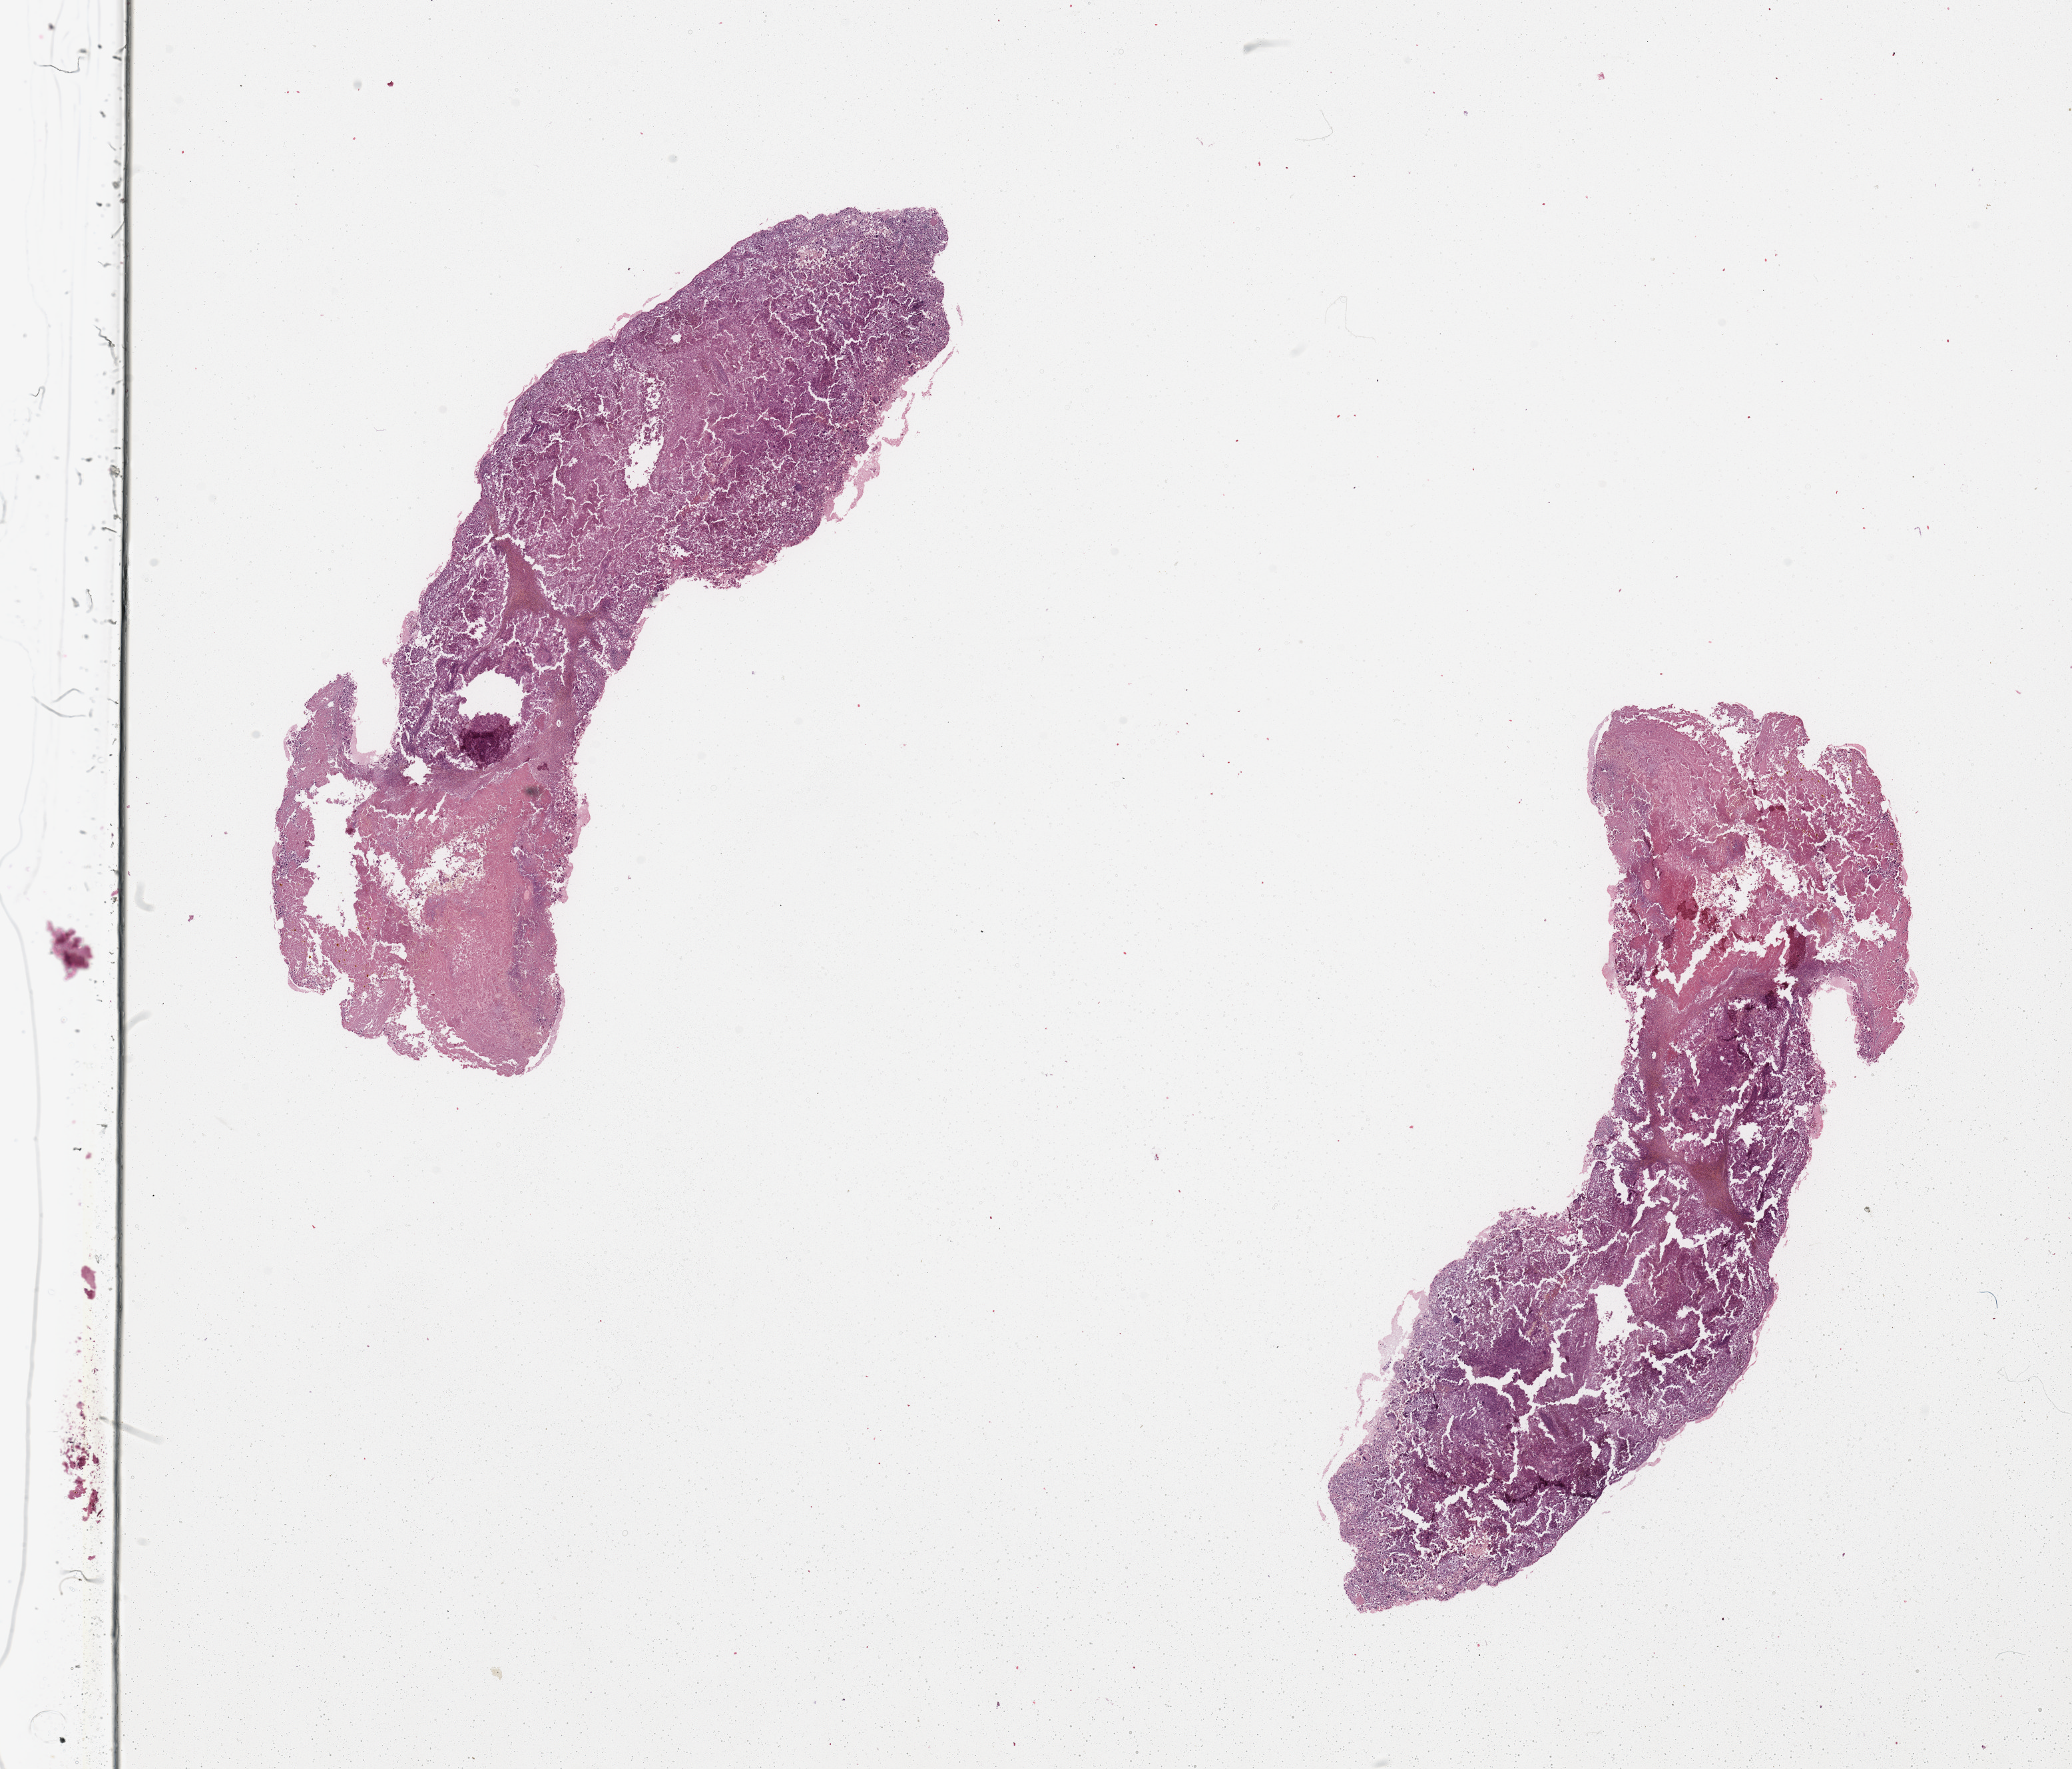
Digitized H&E-stained tissue section (whole slide), whole scanned area (about 24.6 x 21.0 mm, slide scanned at 20x) shown as a low-resolution overview. Melanoma tumour tissue; sampled site not recorded. Male, 33 y/o.
Diagnosis: Malignant melanoma, NOS.